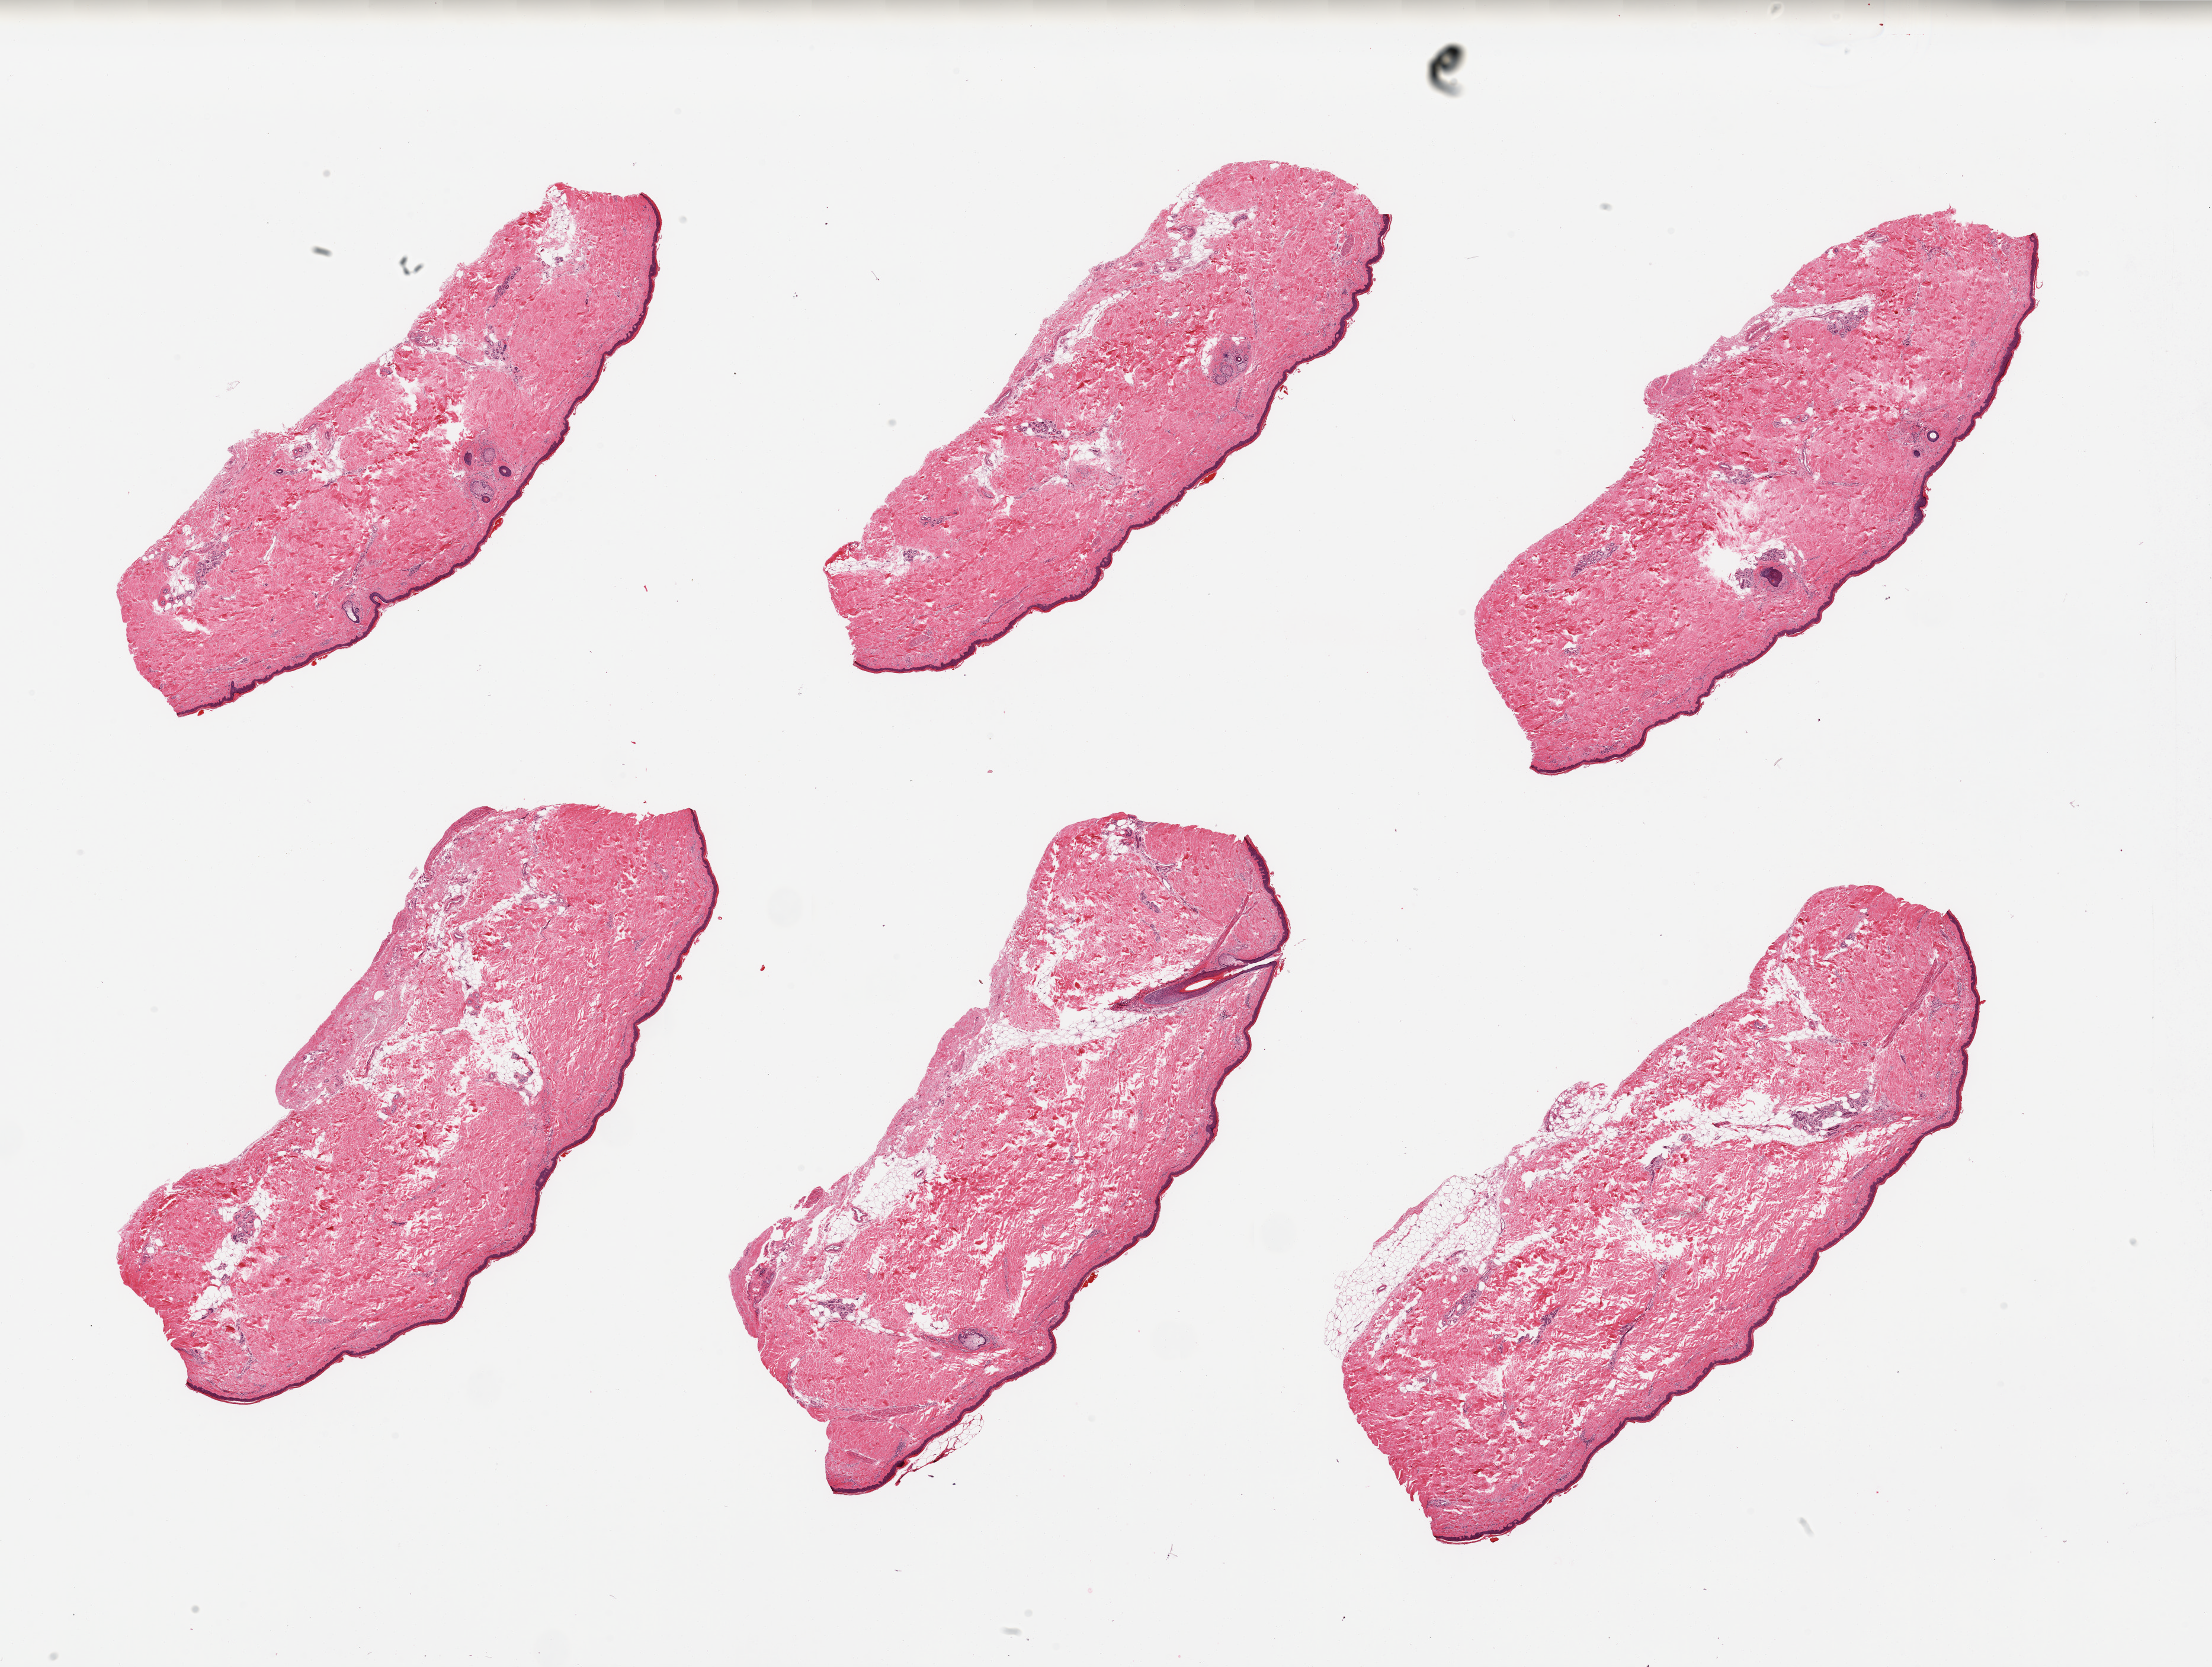
Haematoxylin and eosin whole-slide image — shown as a low-resolution overview of the whole scanned area (about 29.5 x 22.3 mm, from a 20x scan), PAXgene-fixed paraffin-embedded (PFPE) section, target tissue: skin of lower leg, tissue donor sample. Male donor.
* pathologist's review note for this sample: 6 pieces; ~10 - 20% interstitial (periadnexal) fat